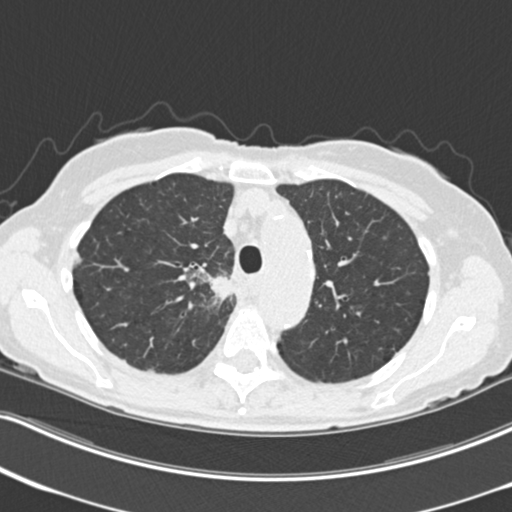
Chest CT (low-dose screening protocol), one axial image, third annual screen, lung window (W 1500 / L -600 HU), 2 mm slice thickness, 512 × 512 image matrix, field of view 322 × 322 mm. Female participant, aged 68 years at enrolment. Current smoker at enrolment.
Expert reader's lesion annotation, bounding box (x1, y1, x2, y2) in pixels: (195, 268, 248, 324). The exam's reader record, not a measurement of the box and not confirmed to be the same lesion: non-calcified nodule or mass ≥4 mm, right upper lobe, 31 × 29 mm, poorly defined margins, soft tissue attenuation, pre-existing on the prior screen: no.